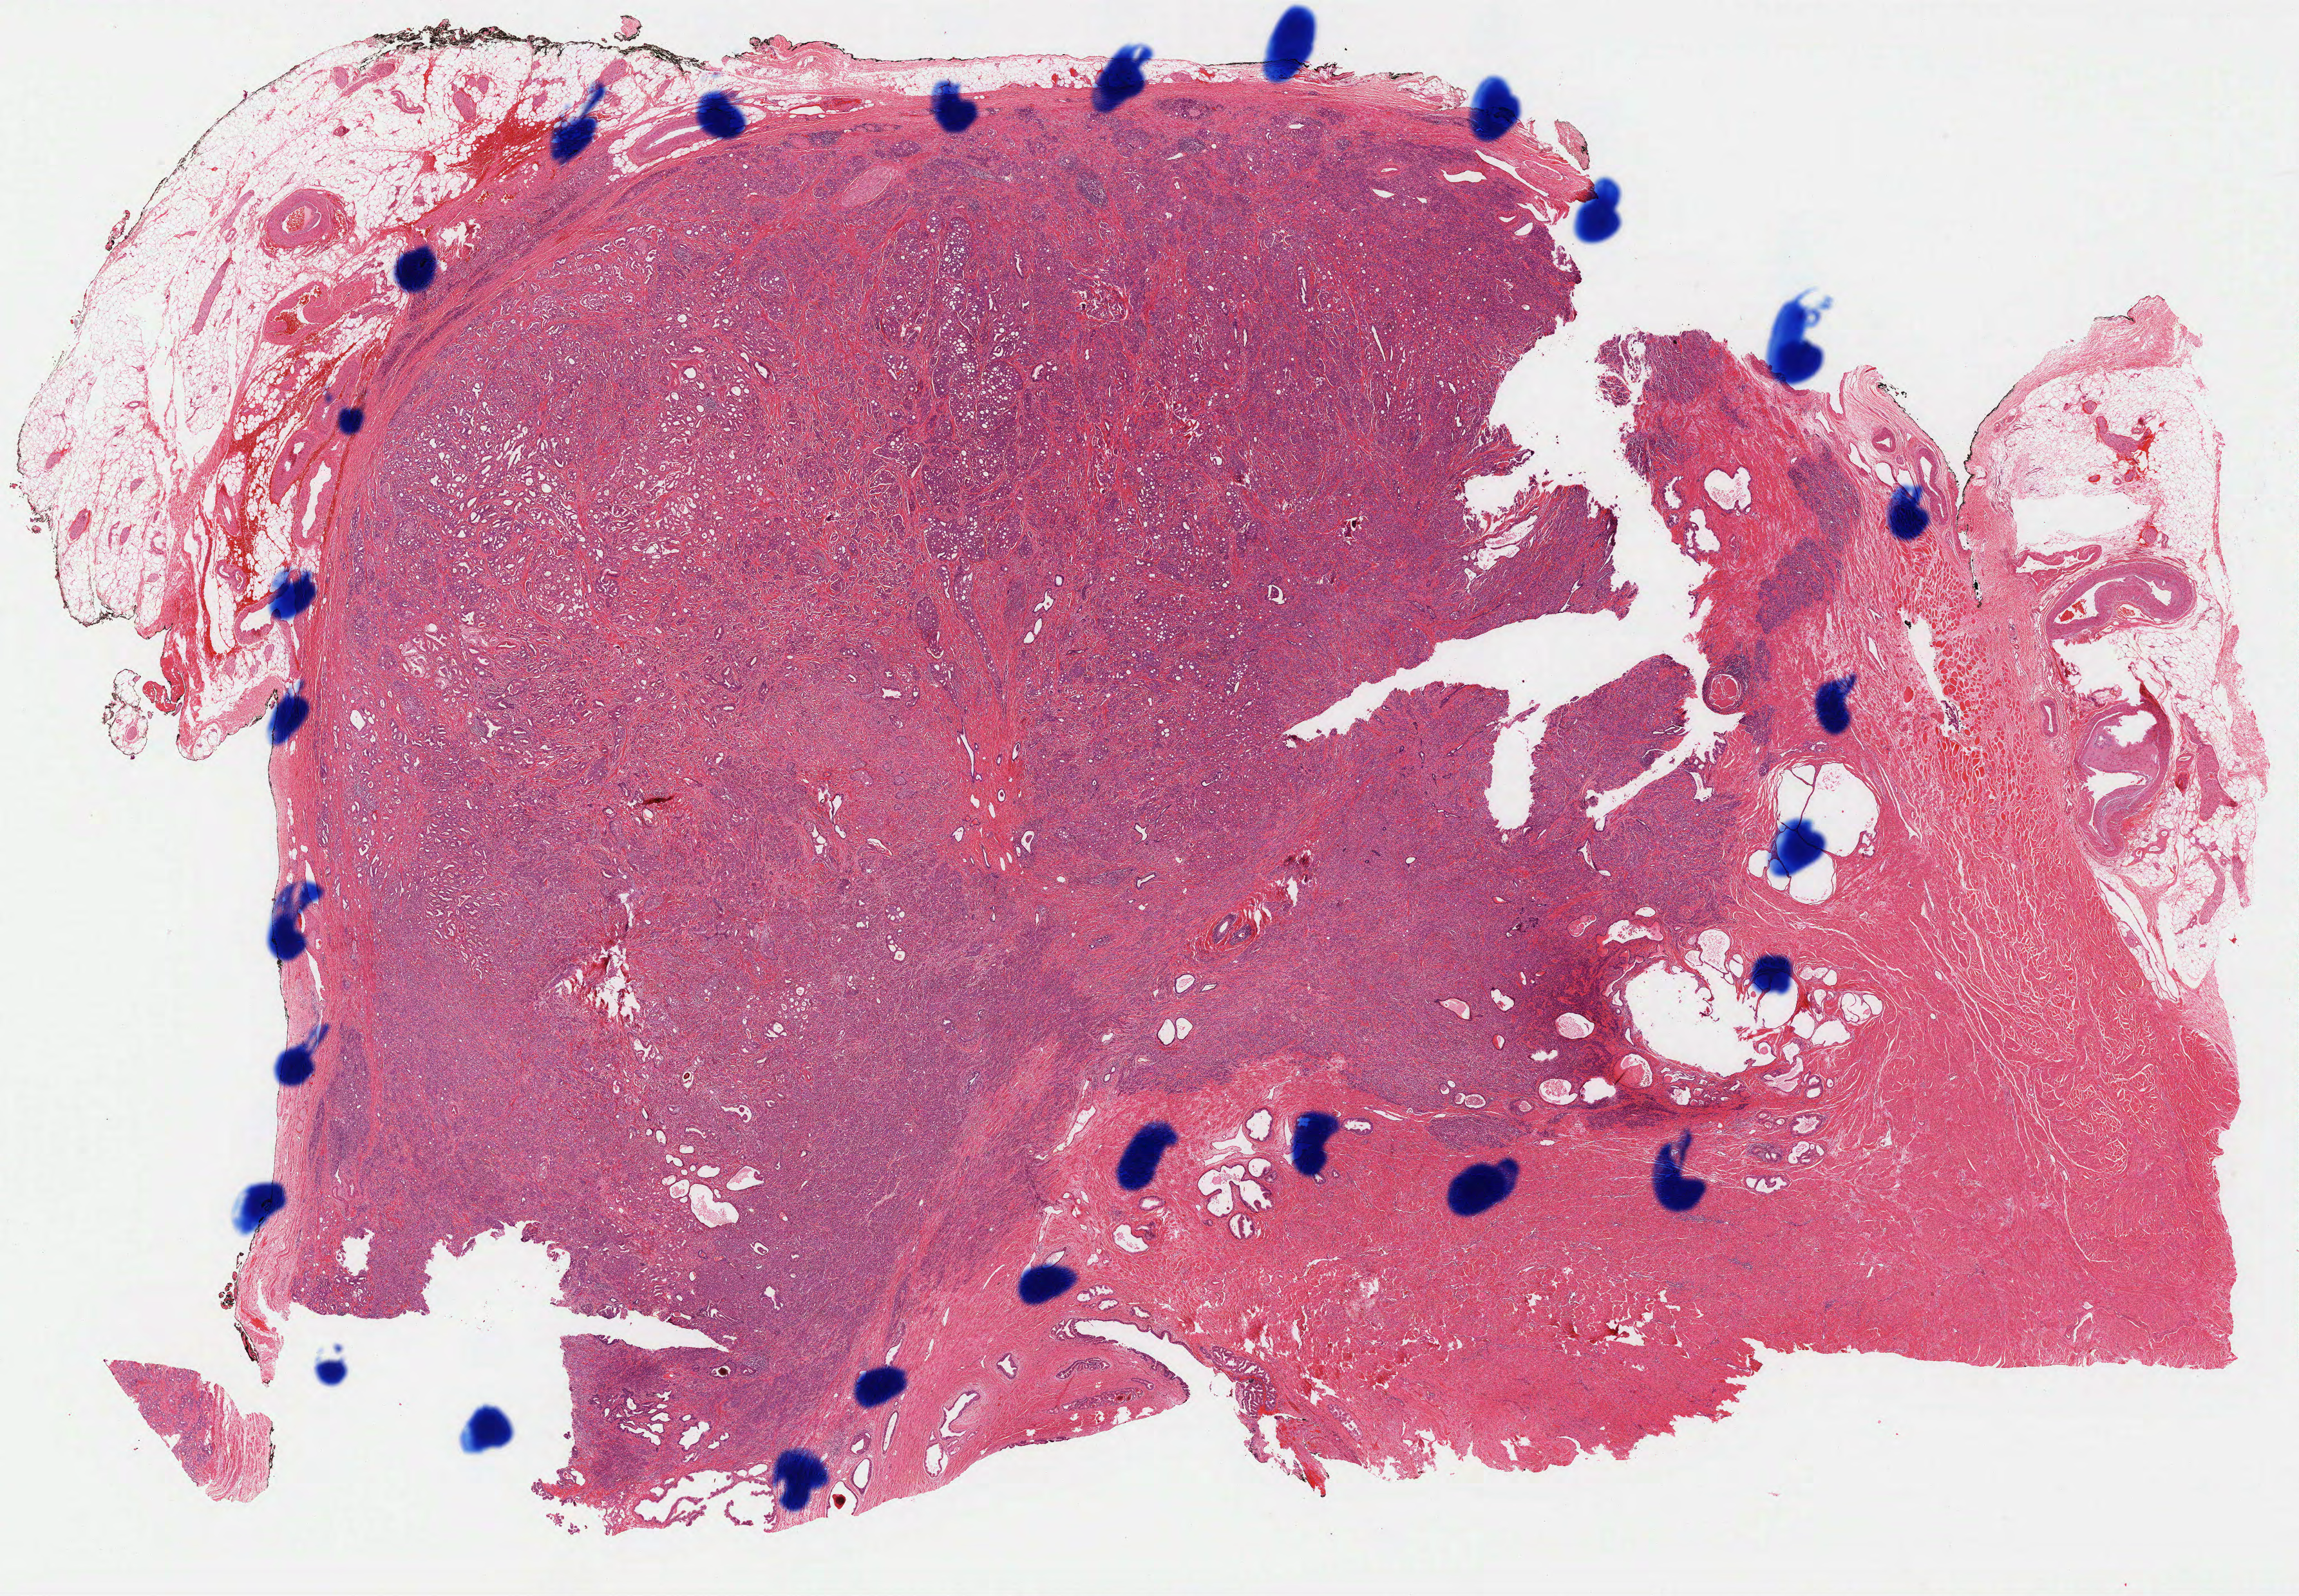
H&E whole-slide image, shown as a low-resolution overview of the whole scanned area (about 28.6 x 19.8 mm, slide scanned at 40x). Formalin-fixed paraffin-embedded (FFPE) diagnostic section. Prostate, primary tumour sample. Male patient; age at initial diagnosis 54 years. Gleason score: 9 (4+5).
Lymph nodes positive (case pathology): 3 of 12 examined. Laterality: bilateral. Histologic diagnosis: Adenocarcinoma, NOS (prostate gland).